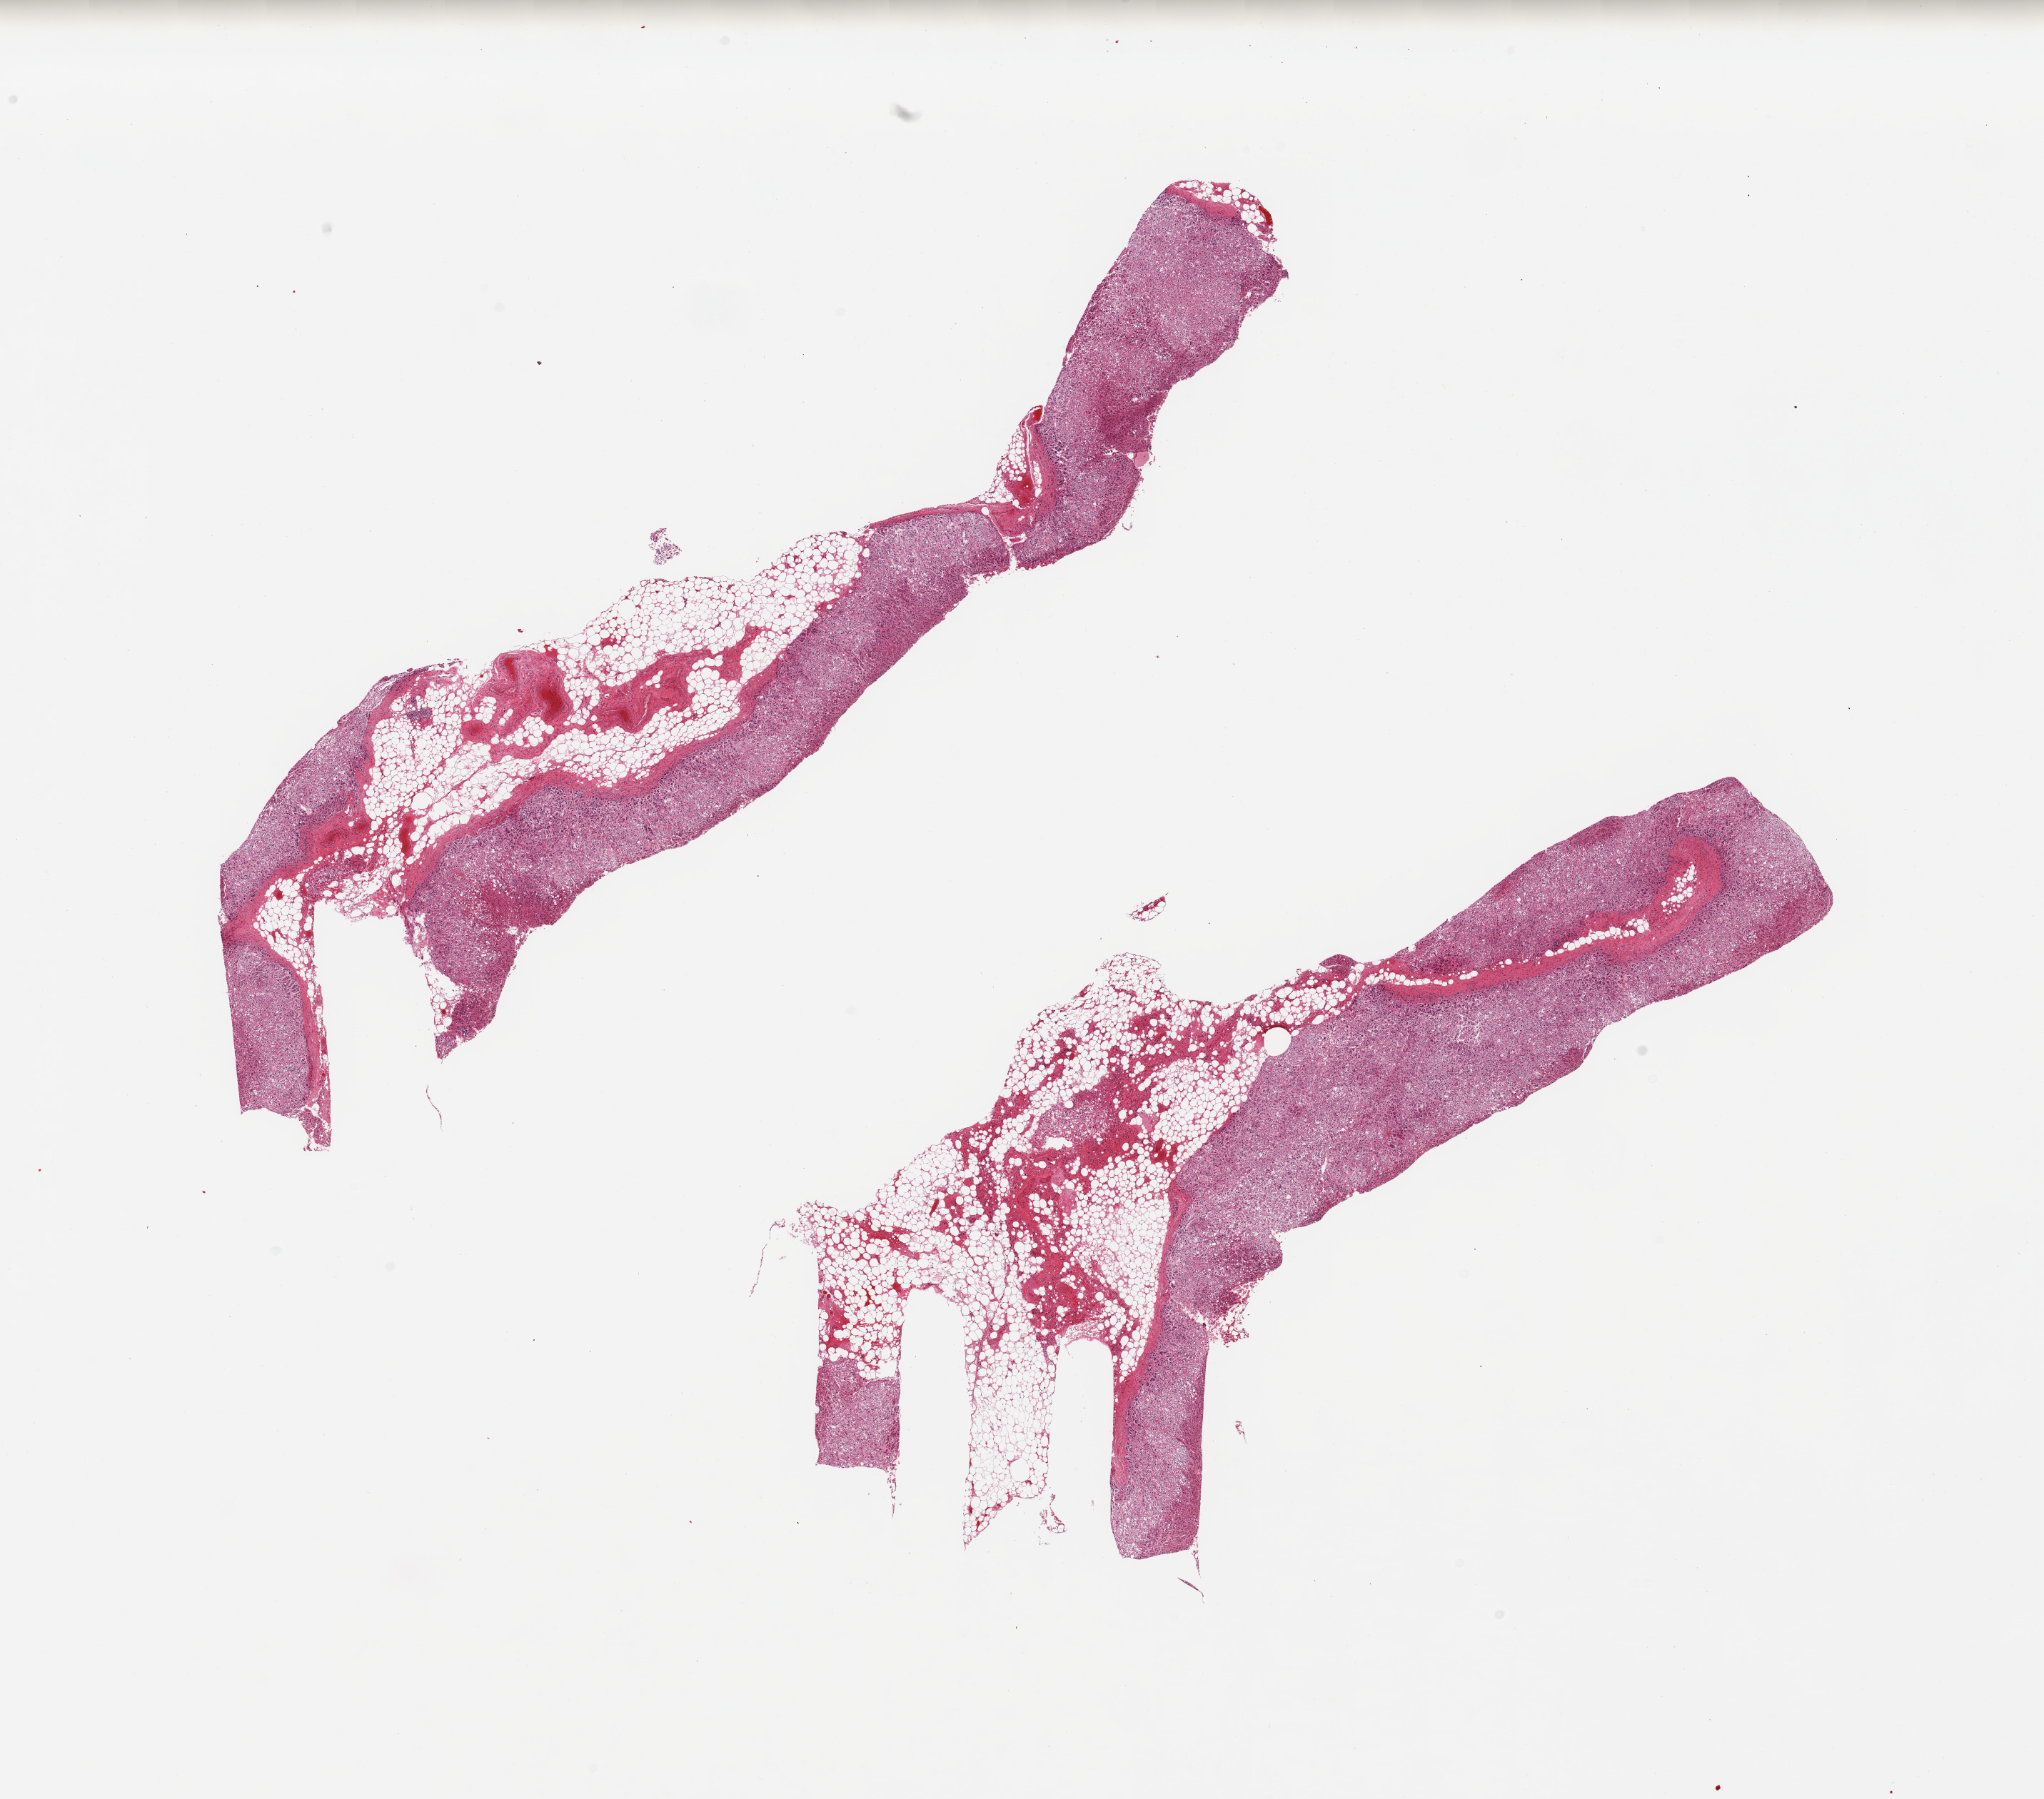
Digitized haematoxylin and eosin-stained section, brightfield — low-resolution overview of the scanned area, about 22.6 x 19.9 mm (slide scanned at 20x), PAXgene-fixed, paraffin-embedded tissue, sampled site (target tissue): adrenal gland, tissue donor sample. Donor sex: female.
• pathologist's review note for this sample: 2 pieces, each is ~50% fat